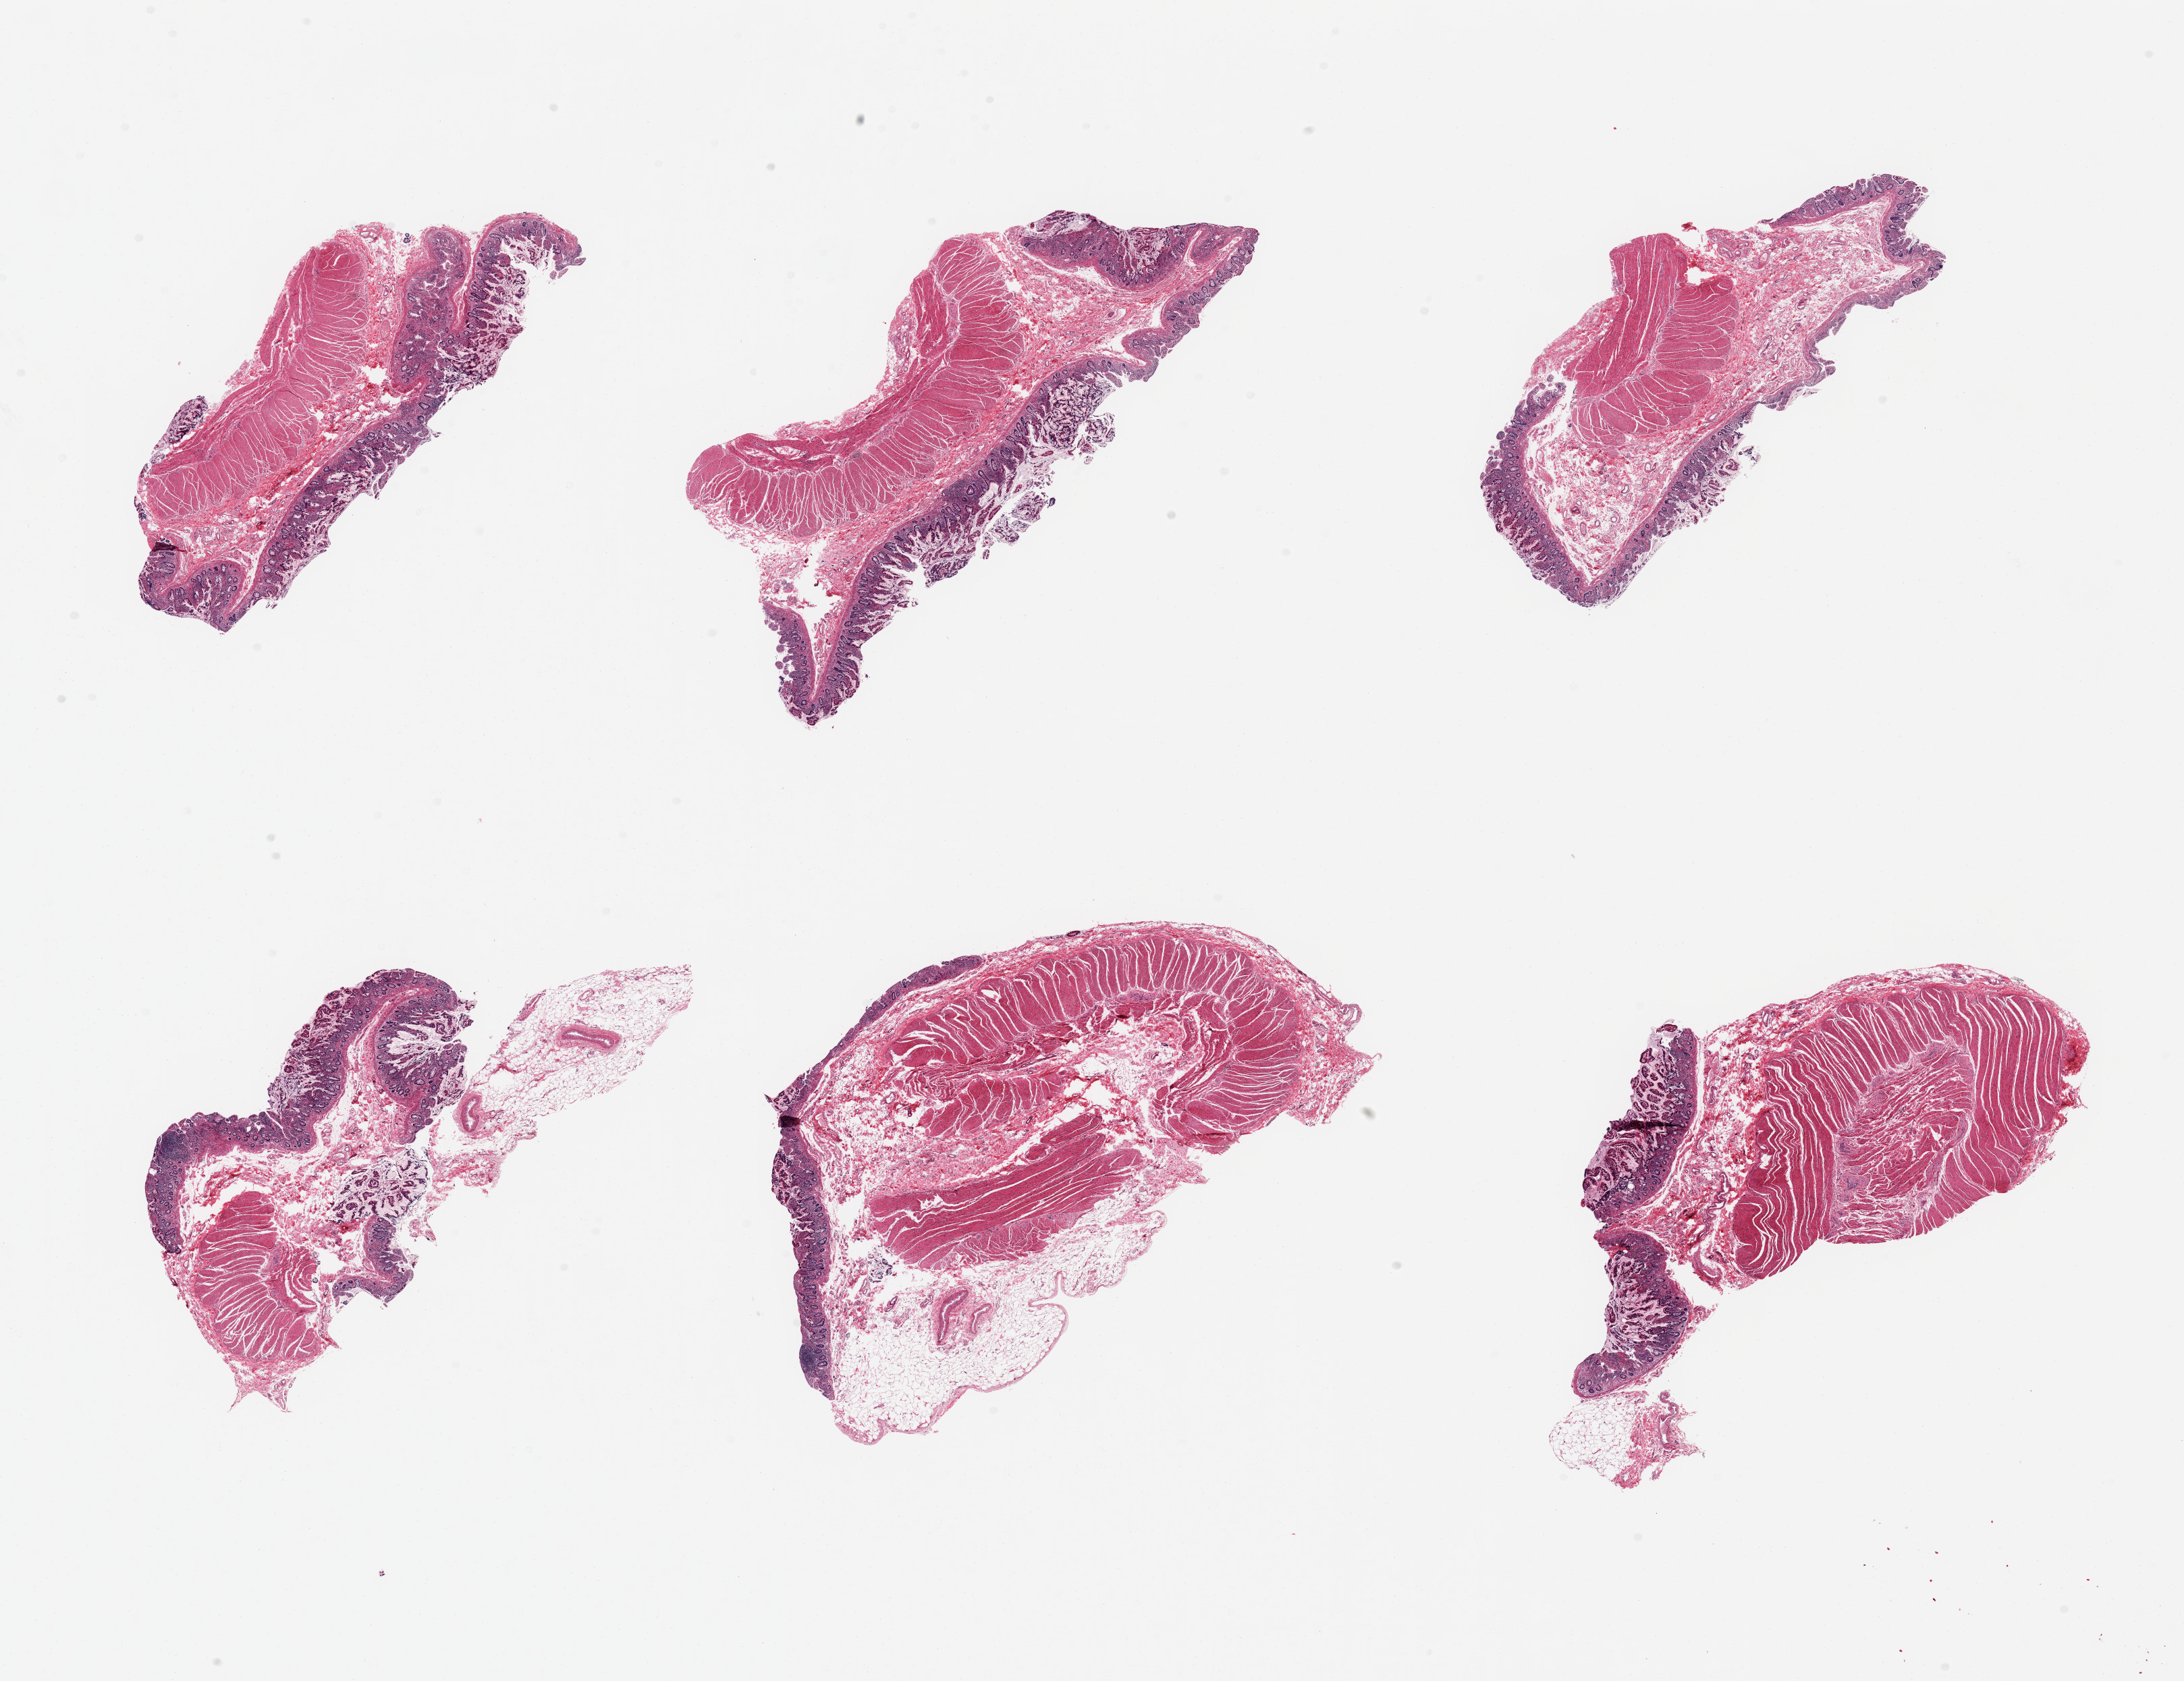
Hematoxylin and eosin (H&E) whole-slide image, brightfield, a low-resolution overview of the entire scanned area, about 25.6 x 19.7 mm; PAXgene-fixed, paraffin-embedded tissue; sampled site (target tissue): ileum; tissue donor sample. Male donor.
Review note (as recorded): 6 pieces, few lymphoid glandular aggregates.